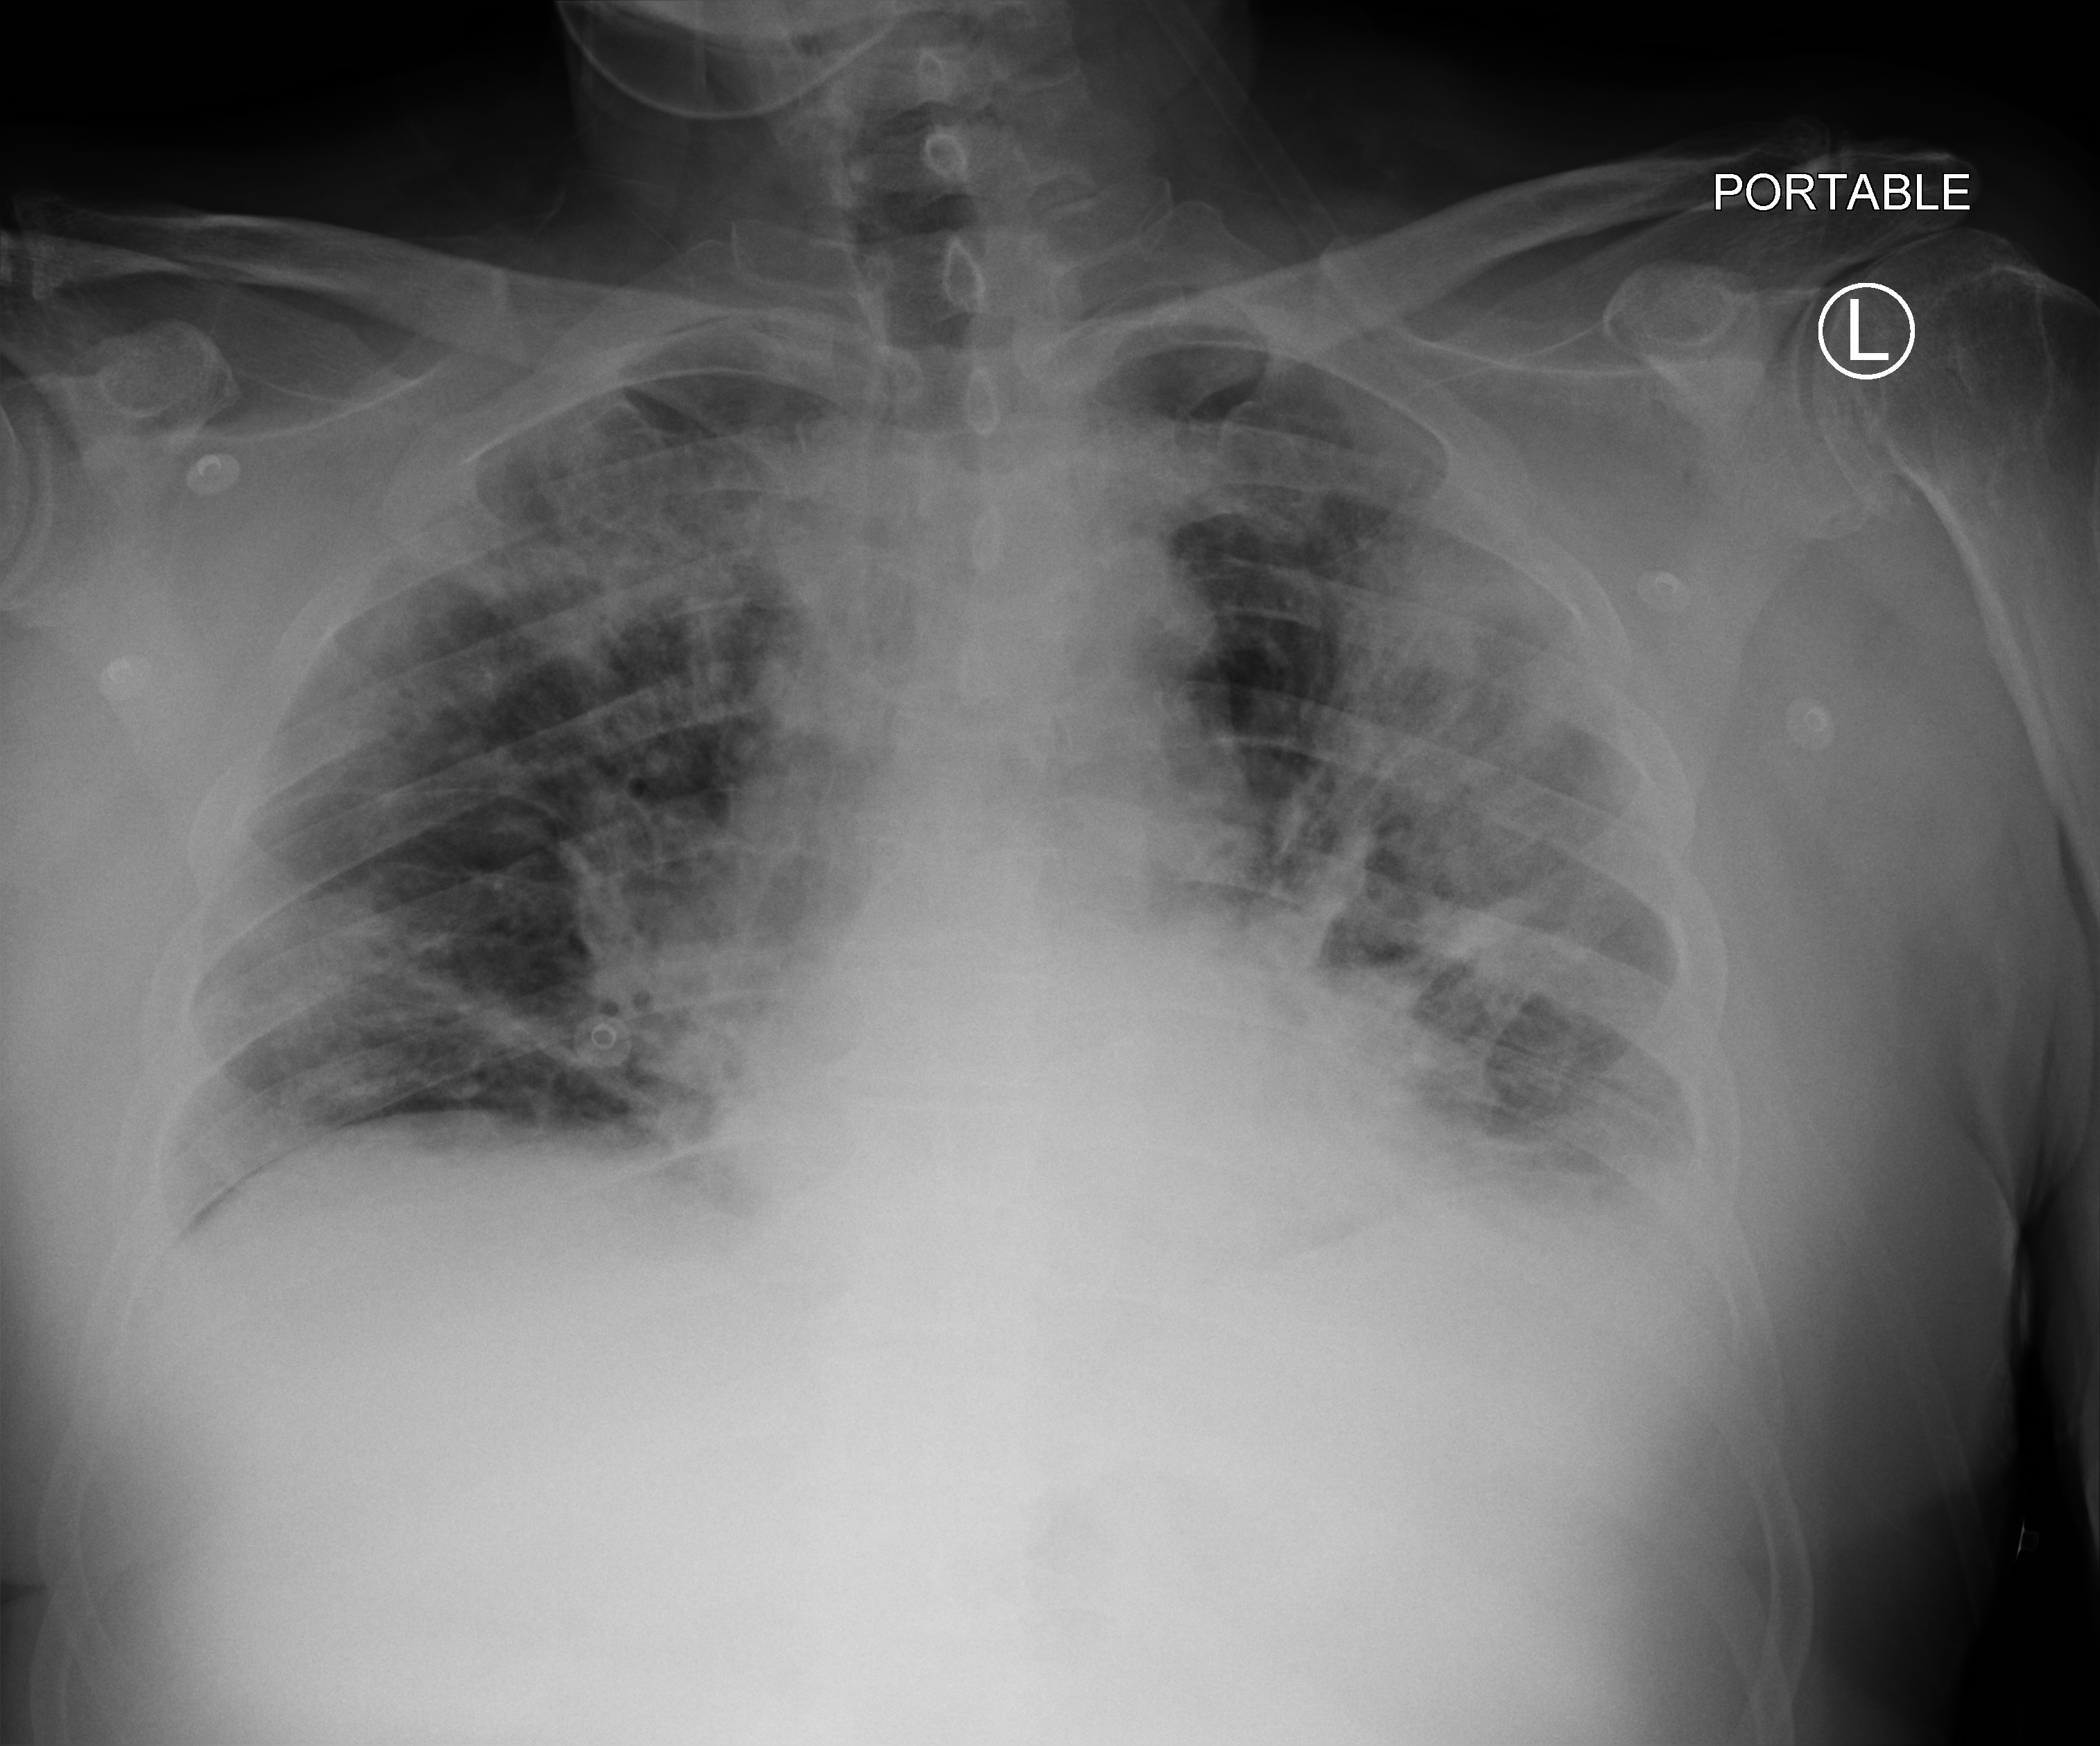
Chest X-ray (portable); anteroposterior (AP) projection. Patient hospitalised with COVID-19; male, aged 60–74 years.
Hospital-stay facts (about this admission, not read from this image; timing relative to this image not recorded): mechanically ventilated during this hospital stay: no; admitted to intensive care during this hospital stay: no; hypertension (admission record): no.